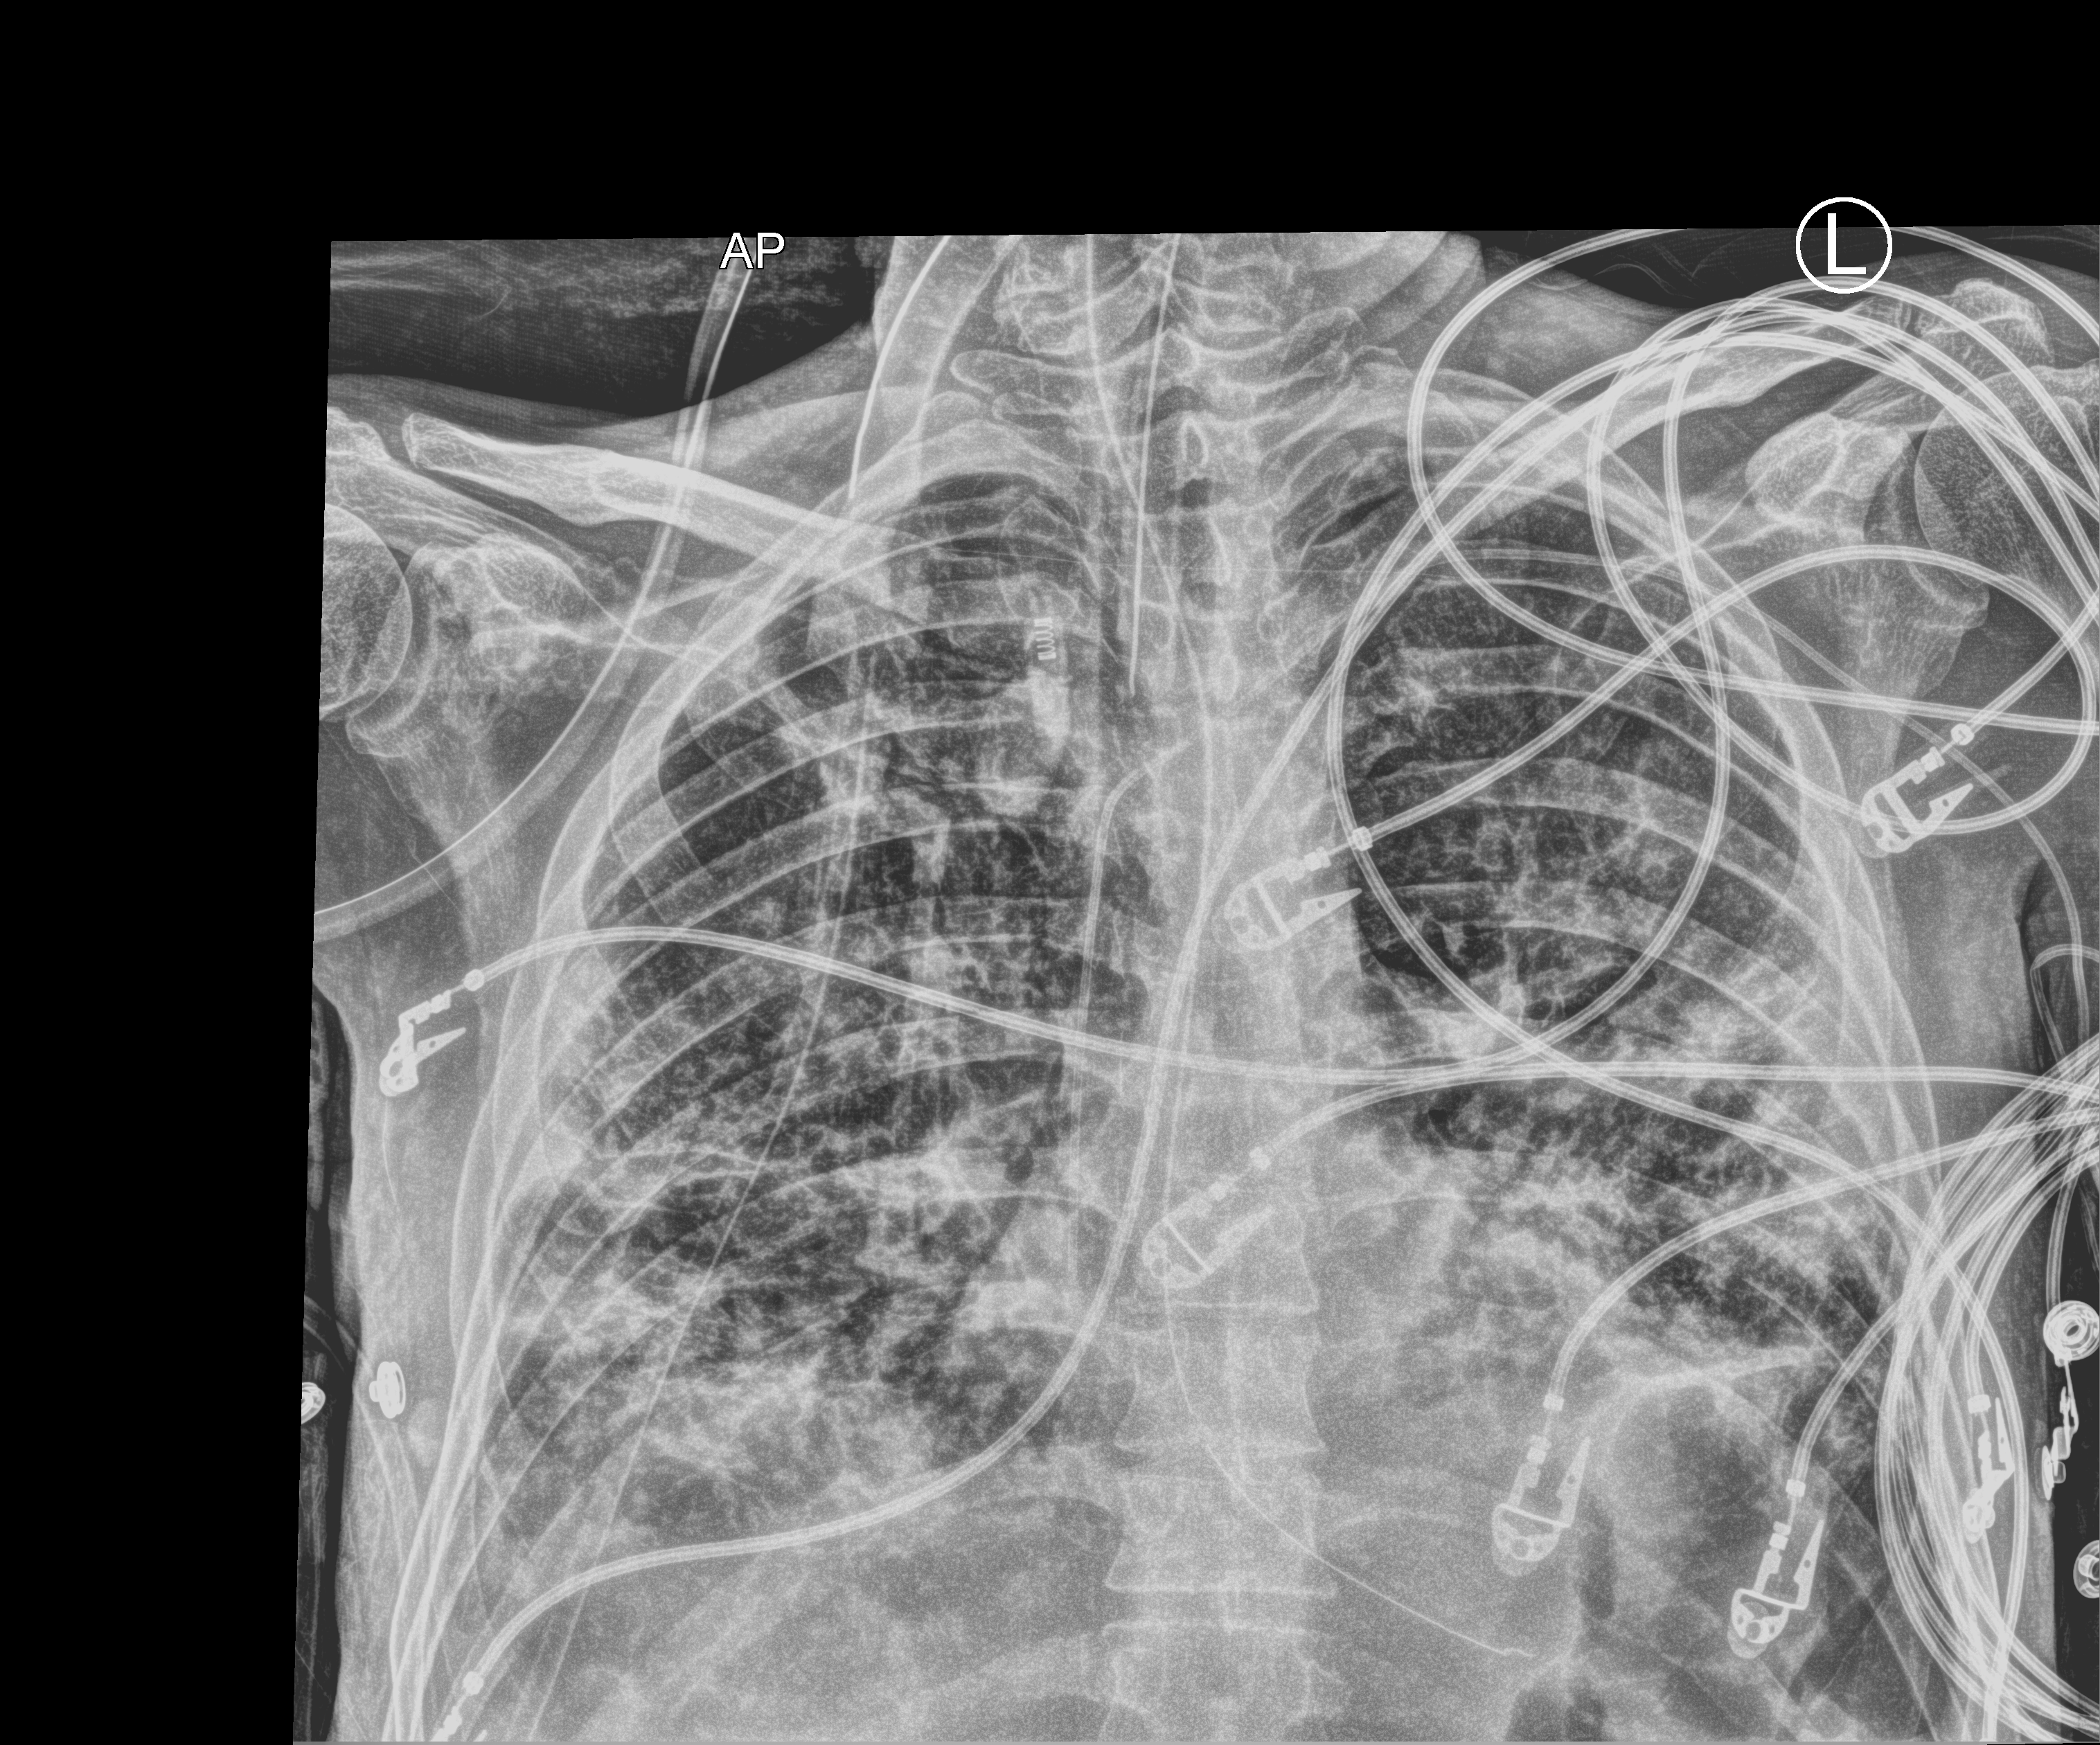
Chest X-ray (portable); anteroposterior (AP) projection. Male patient hospitalised with COVID-19, age 18–59 years.
Admission-level facts for this patient (not findings on this image; timing relative to this image not recorded): admitted to intensive care during this hospital stay: yes; other chronic lung disease (admission record): no; mechanically ventilated during this hospital stay: yes.